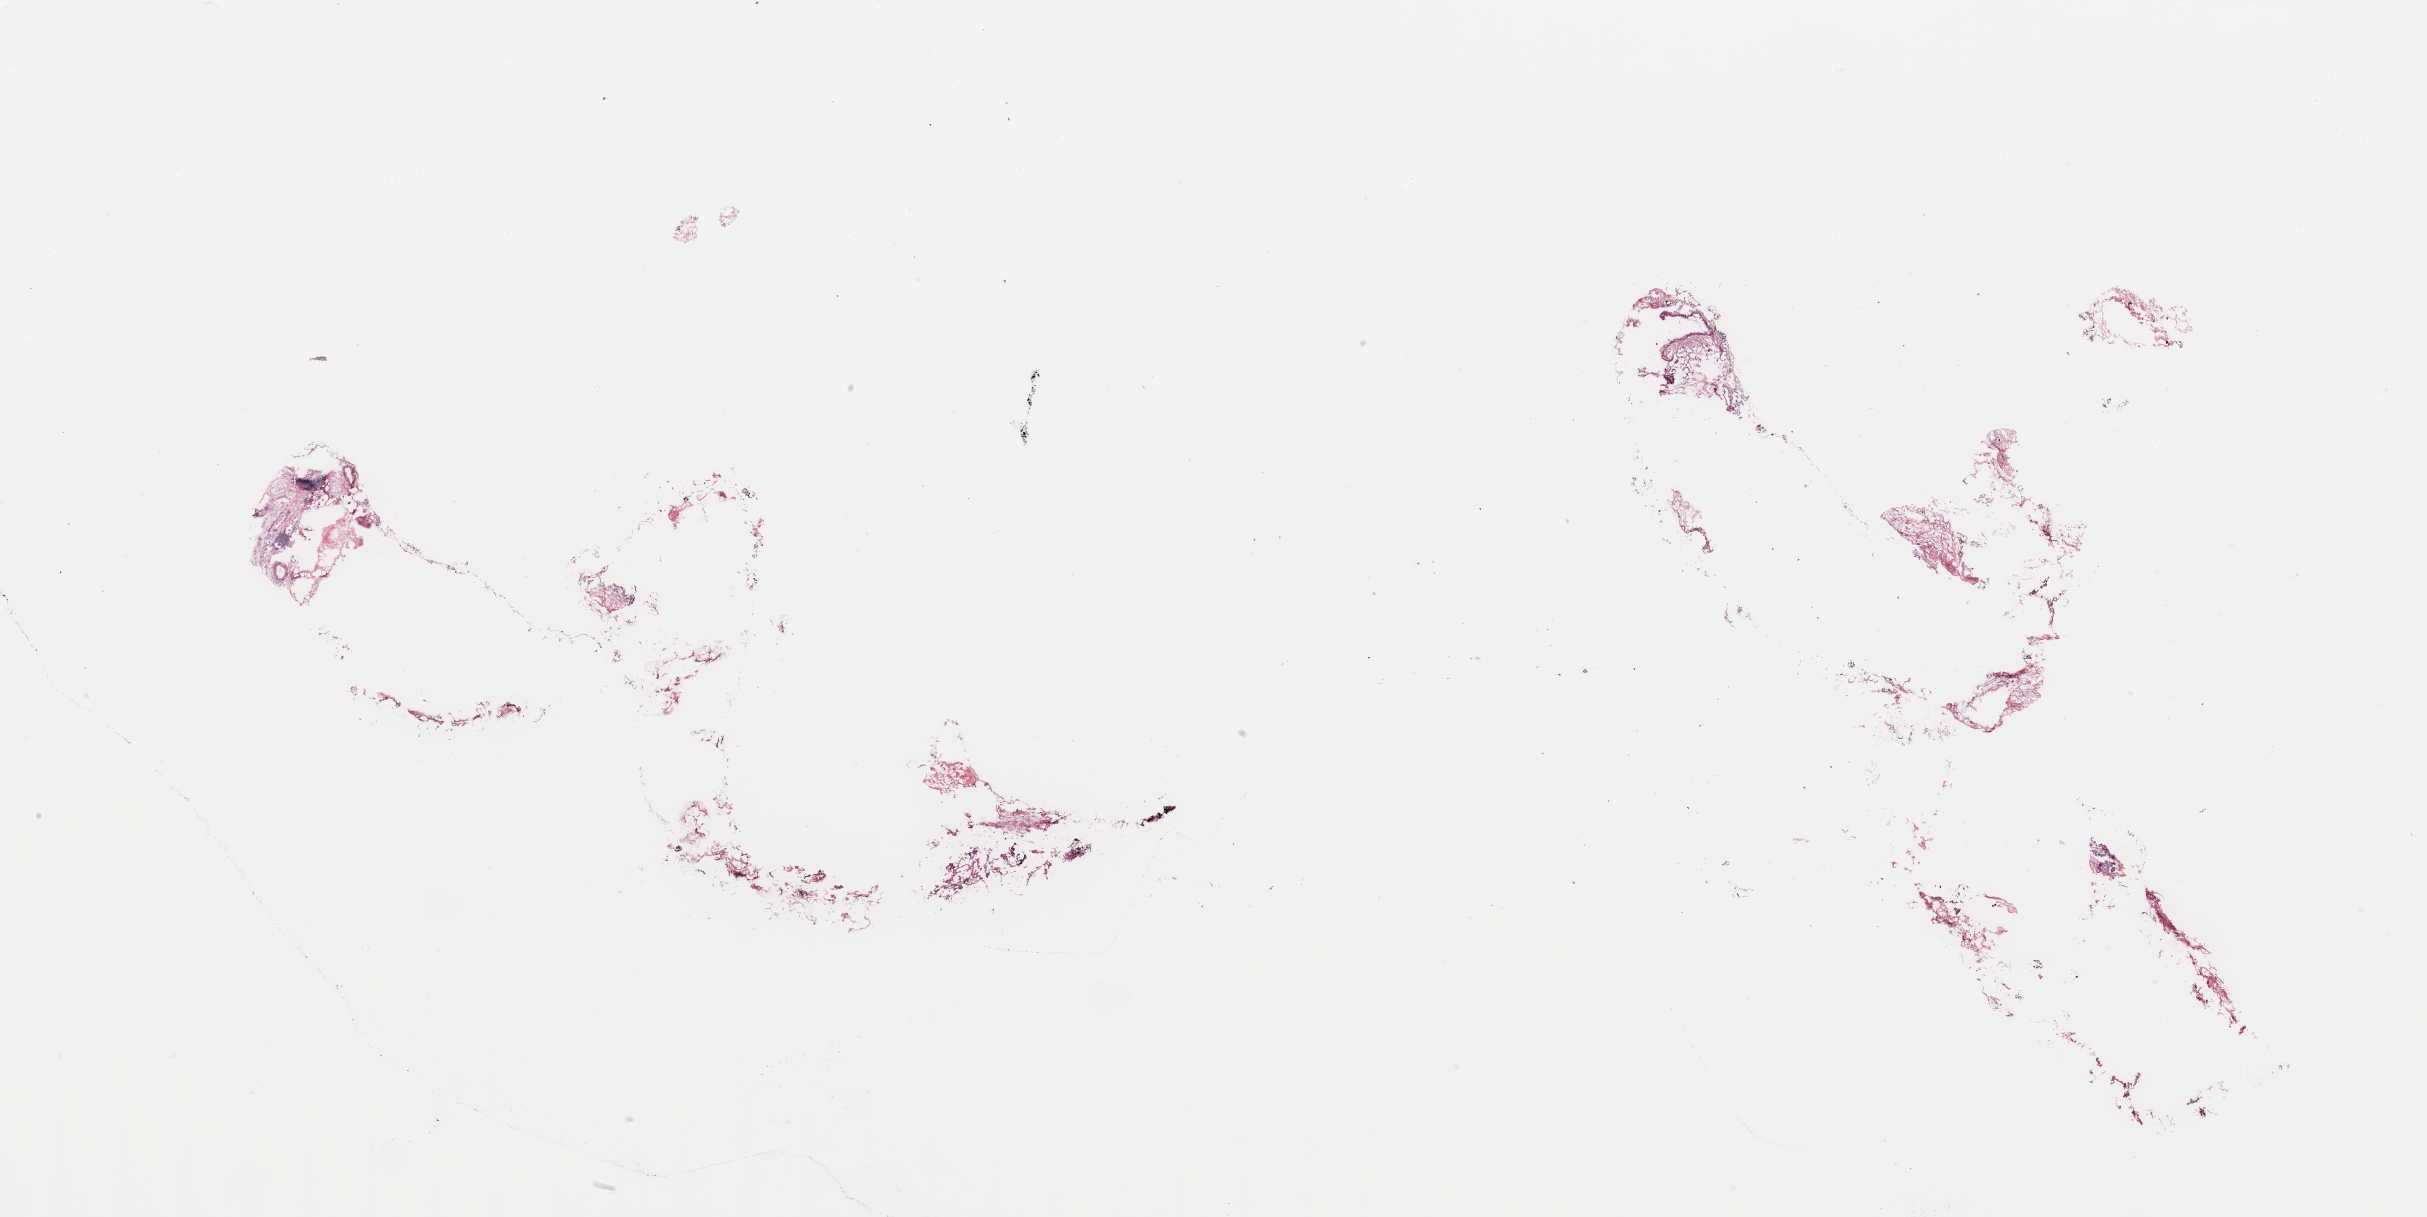
Whole-slide histology image, H&E-stained, shown as a low-resolution overview of the whole scanned area (about 38.4 x 19.3 mm, acquisition: 20x scan), tumour tissue sample, breast. Female, 58 y/o.
Diagnosis: Infiltrating duct carcinoma, NOS. AJCC pathologic stage: II.